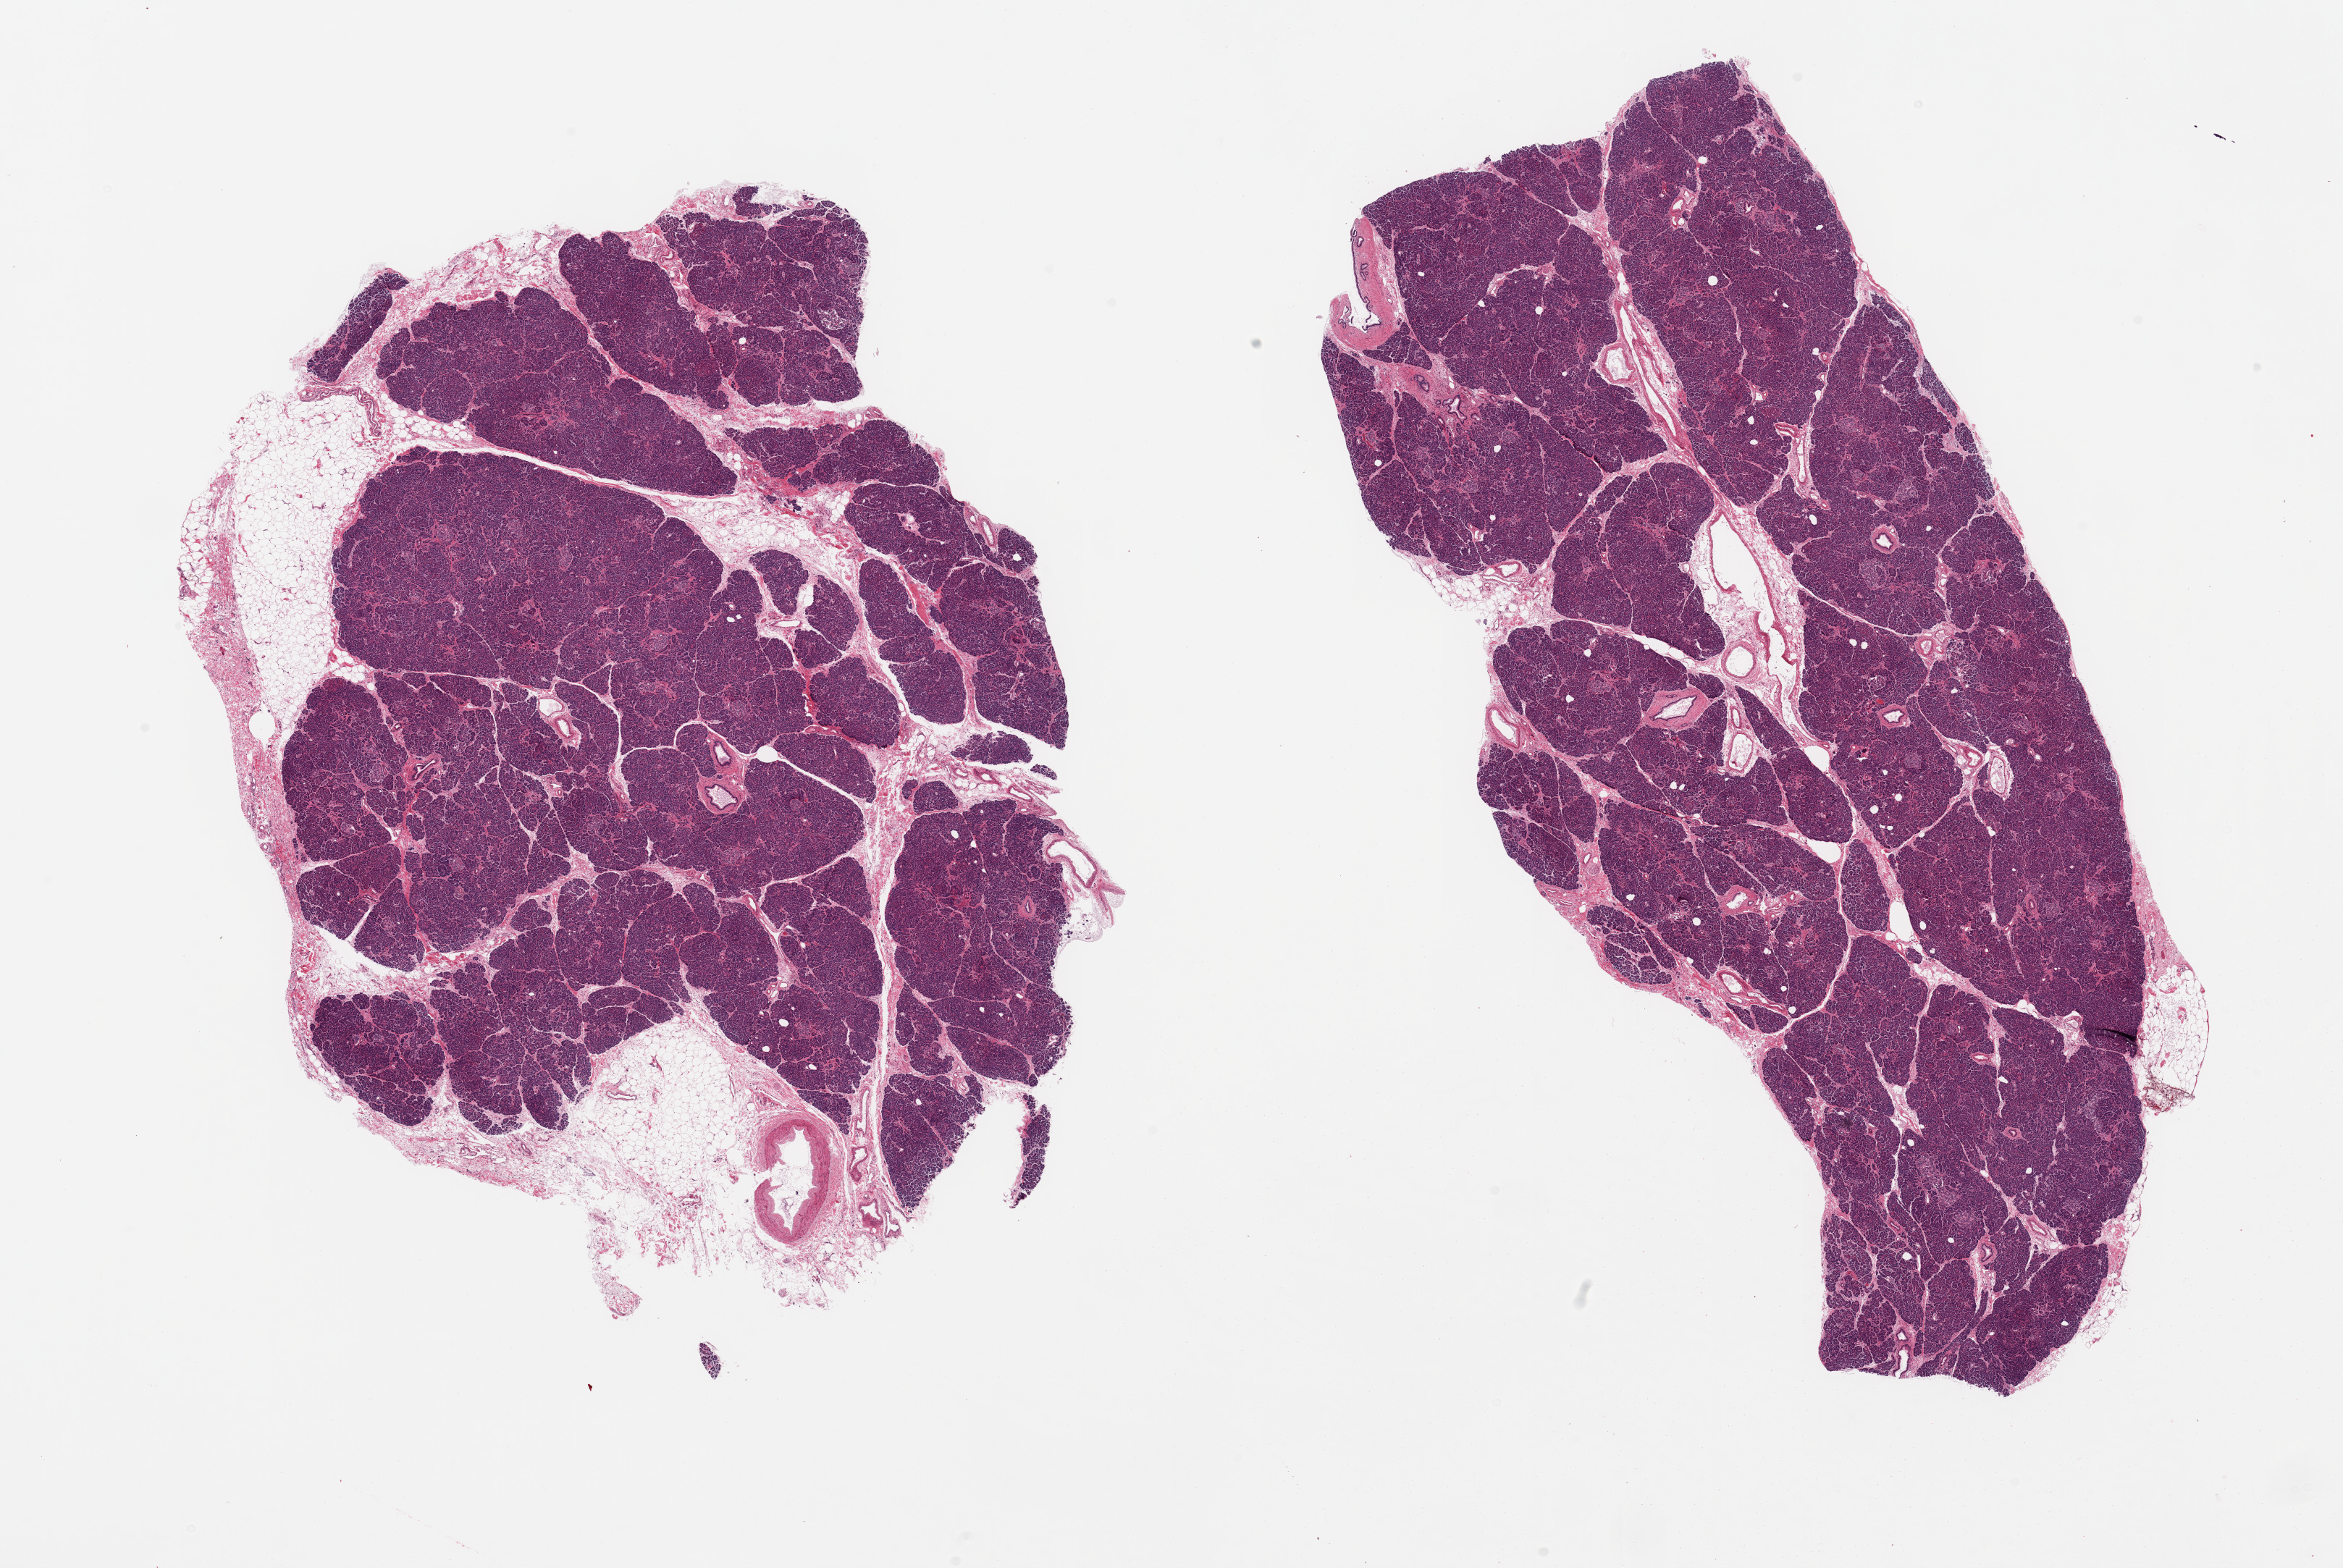
Whole-slide image, H&E stain, brightfield — whole scanned area (about 25.6 x 17.1 mm) shown as a low-resolution overview; PAXgene-fixed paraffin-embedded (PFPE) section; sampled site (target tissue): pancreas; donor tissue sample. Donor sex: female.
- reviewer comment on this tissue sample: 2 pieces; 1 piece has 30% external fat